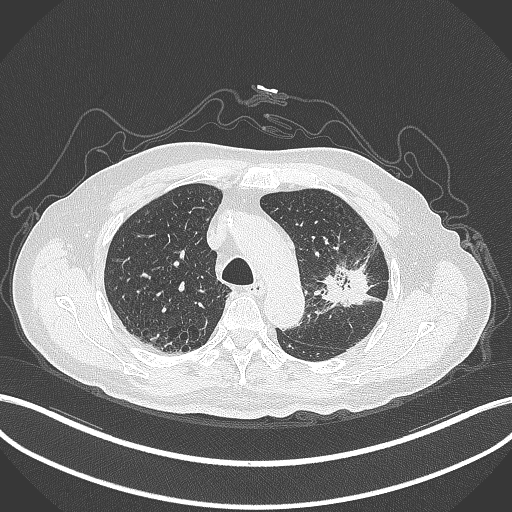
Chest CT, one axial slice; position 217 of 331 along the scan axis; 120 kVp; lung window (W 1500 / L -600 HU); 1 mm slice thickness; 512 × 512 image matrix, field of view 400 × 400 mm. Patient: male, 79 years. Case-level facts recorded for this patient, not image findings: clinical TNM (as recorded): T2a N1 M1; histopathological grade: G3.
Annotated regions visible in this slice (bounding box drawn by a radiologist):
- lung tumour (recorded histology: adenocarcinoma): bounding box (x1, y1, x2, y2) in pixels: (315, 241, 389, 311)